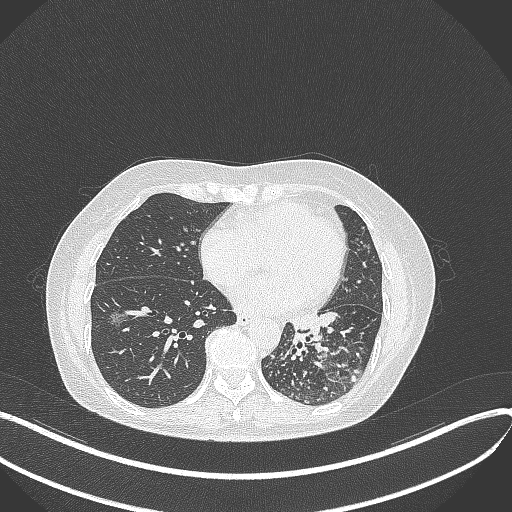
Chest CT, one axial slice; slice 158 of 429 in the series (ordered by position); reconstruction kernel B70f; 100 kVp; lung window (W 1500 / L -600 HU); 1 mm slice thickness; 512 × 512 image matrix, field of view 400 × 400 mm. Patient: female, 63 years. From the clinical record (not read from this slice): clinical TNM (as recorded): T1b N0 M0; histopathological grade: G2-3.
Annotated regions visible in this slice (bounding box drawn by a radiologist):
- lung tumour (recorded histology: adenocarcinoma): bounding box [x1, y1, x2, y2] px = [284, 310, 328, 353]